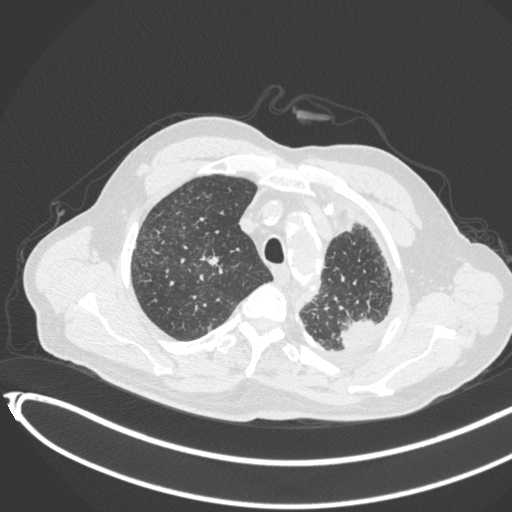
Chest CT, one axial slice; slice 351 of 451 in the series (ordered by position); 120 kVp; lung window (W 1500 / L -600 HU); 1 mm slice thickness; 512 × 512 image matrix, field of view 400 × 400 mm. Male patient, age 78 years. Case-level facts recorded for this patient, not image findings: clinical TNM (as recorded): T1c N0 M1.
Outlined on this slice (bounding box drawn by a radiologist):
- lung tumour (recorded histology: adenocarcinoma): box from (x=334, y=311) to (x=385, y=357) px